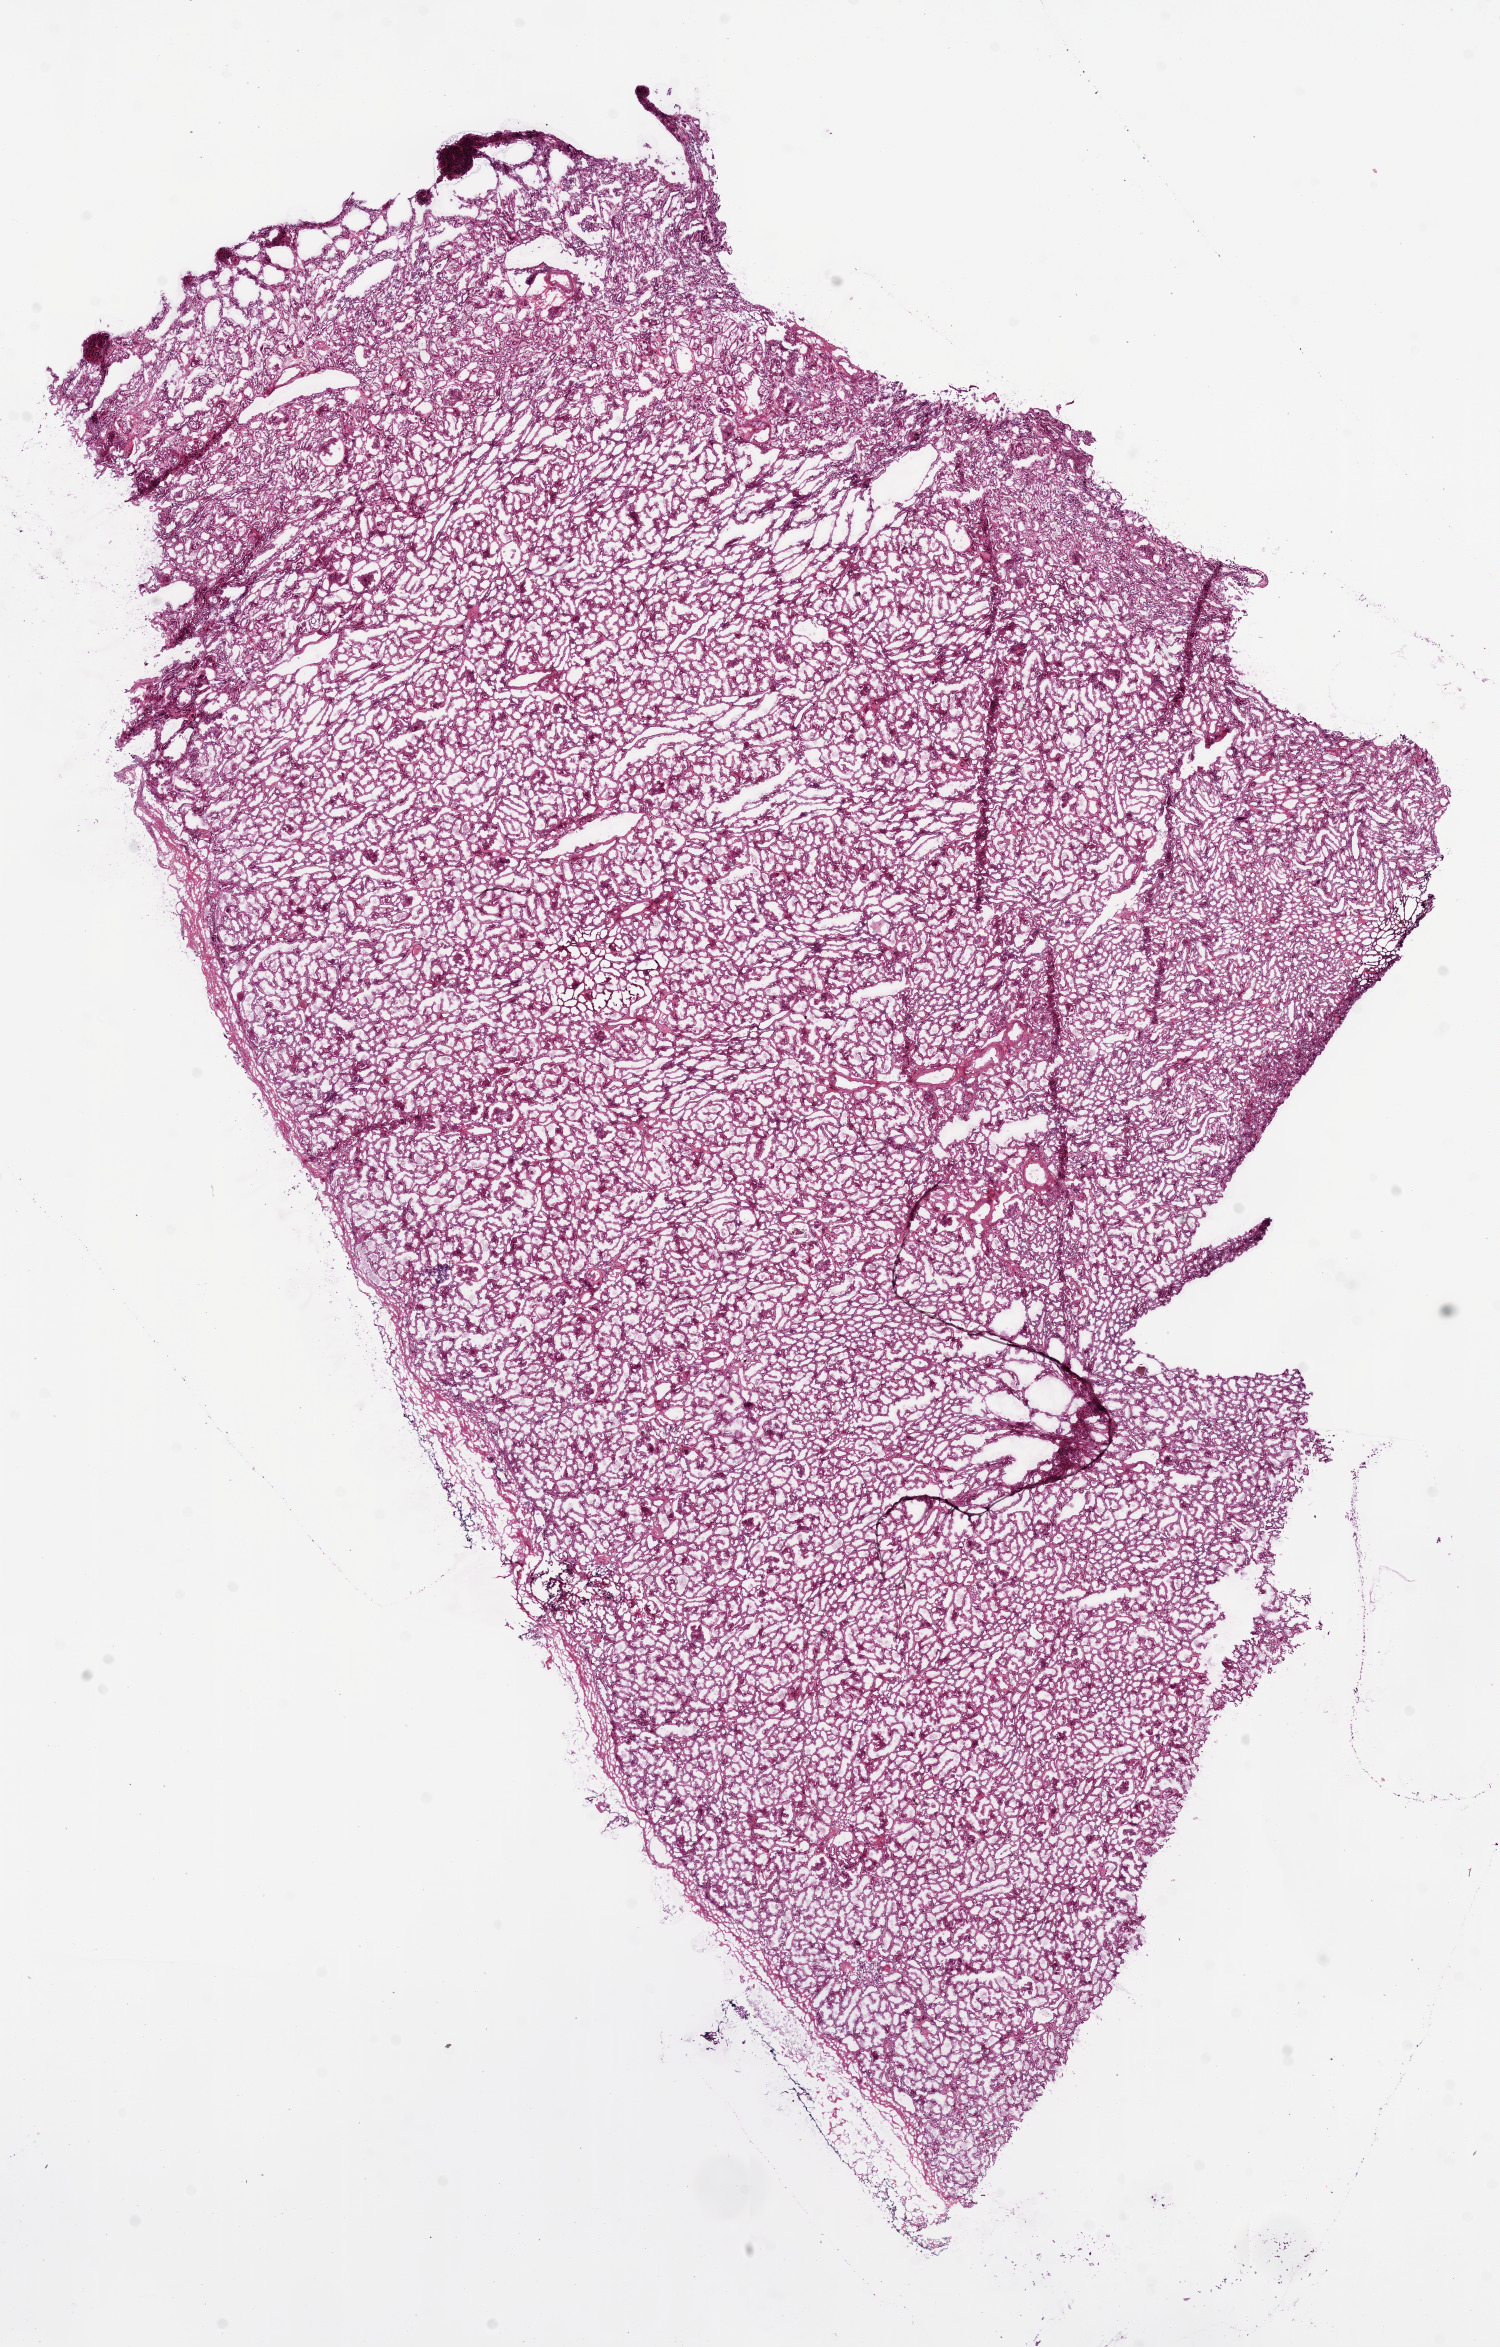
Hematoxylin and eosin (H&E) stained whole-slide image, whole scanned area (about 12.0 x 18.8 mm) shown as a low-resolution overview; frozen section from the bottom of the tissue portion; solid tissue normal (non-tumour tissue) sample from the kidney. Patient: female, age at initial diagnosis 82 years.
This section: solid tissue normal sample (biorepository sample class). Patient diagnosis: Clear cell adenocarcinoma, NOS.